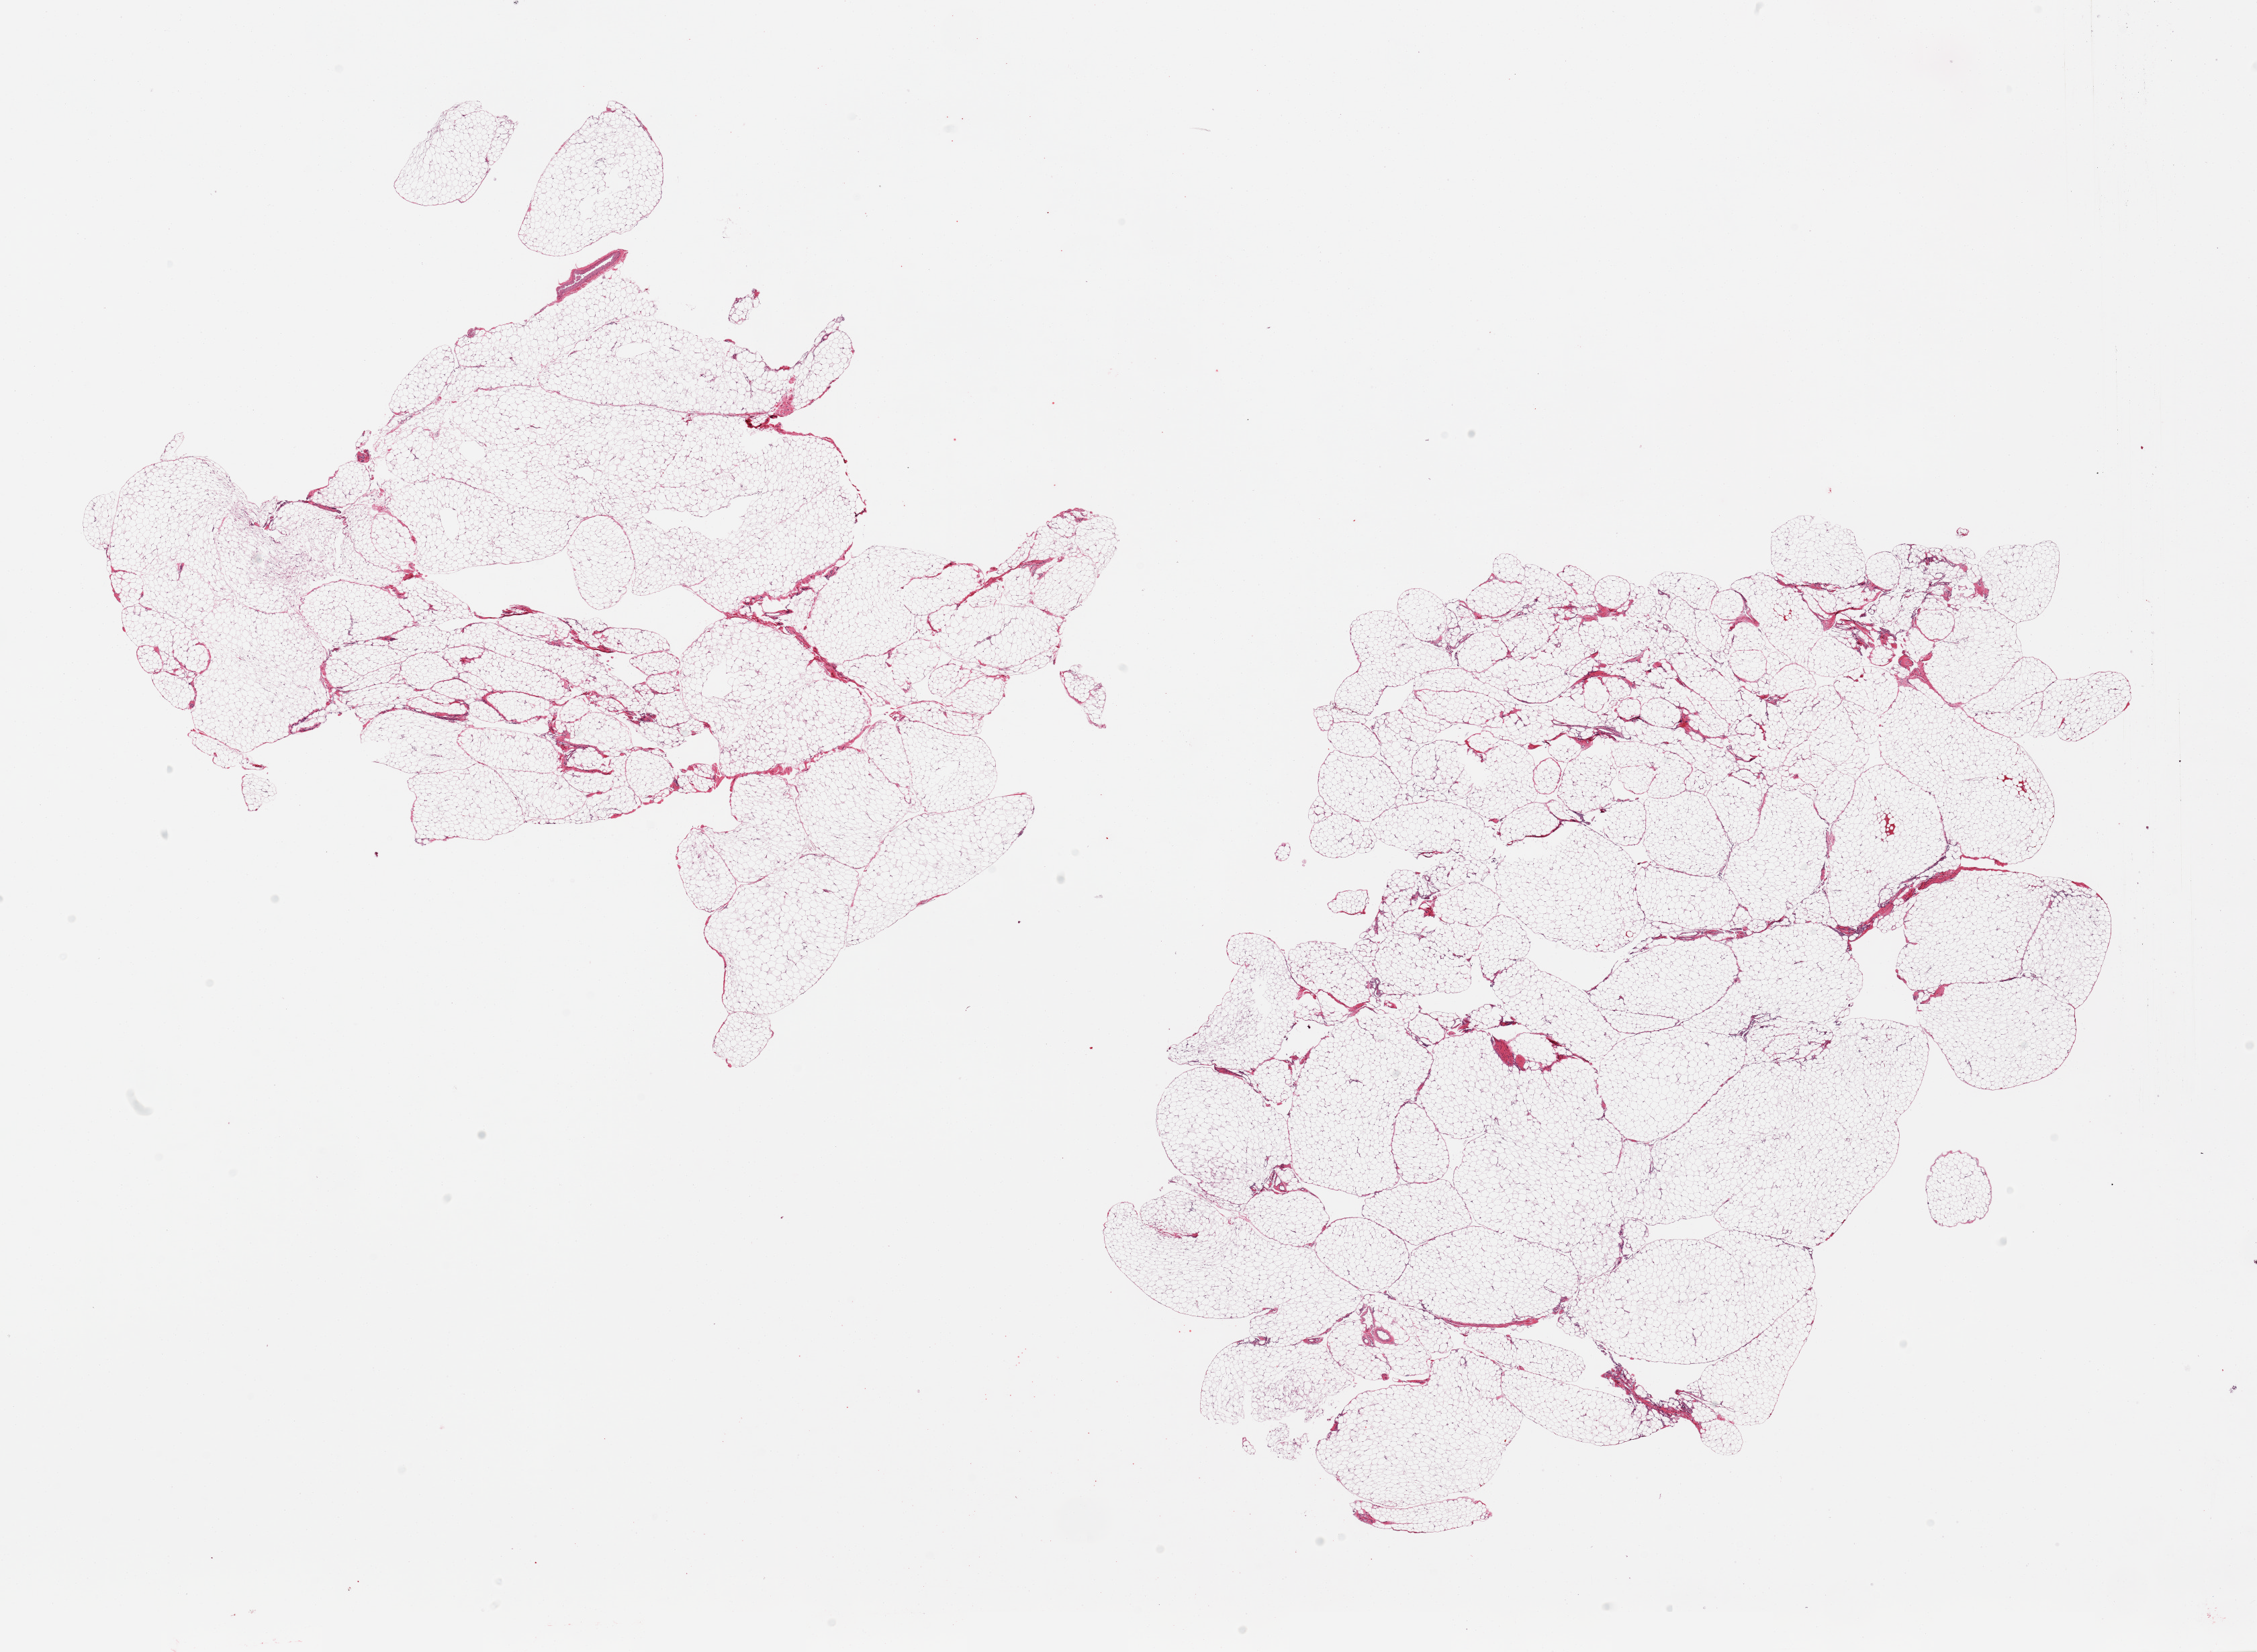
Digitized hematoxylin and eosin (H&E)-stained section, whole scanned area (about 26.6 x 19.5 mm) shown as a low-resolution overview; PAXgene-fixed paraffin-embedded (PFPE) section; sampled site (target tissue): omentum; tissue donor sample.
* review note (as recorded): 2 pieces